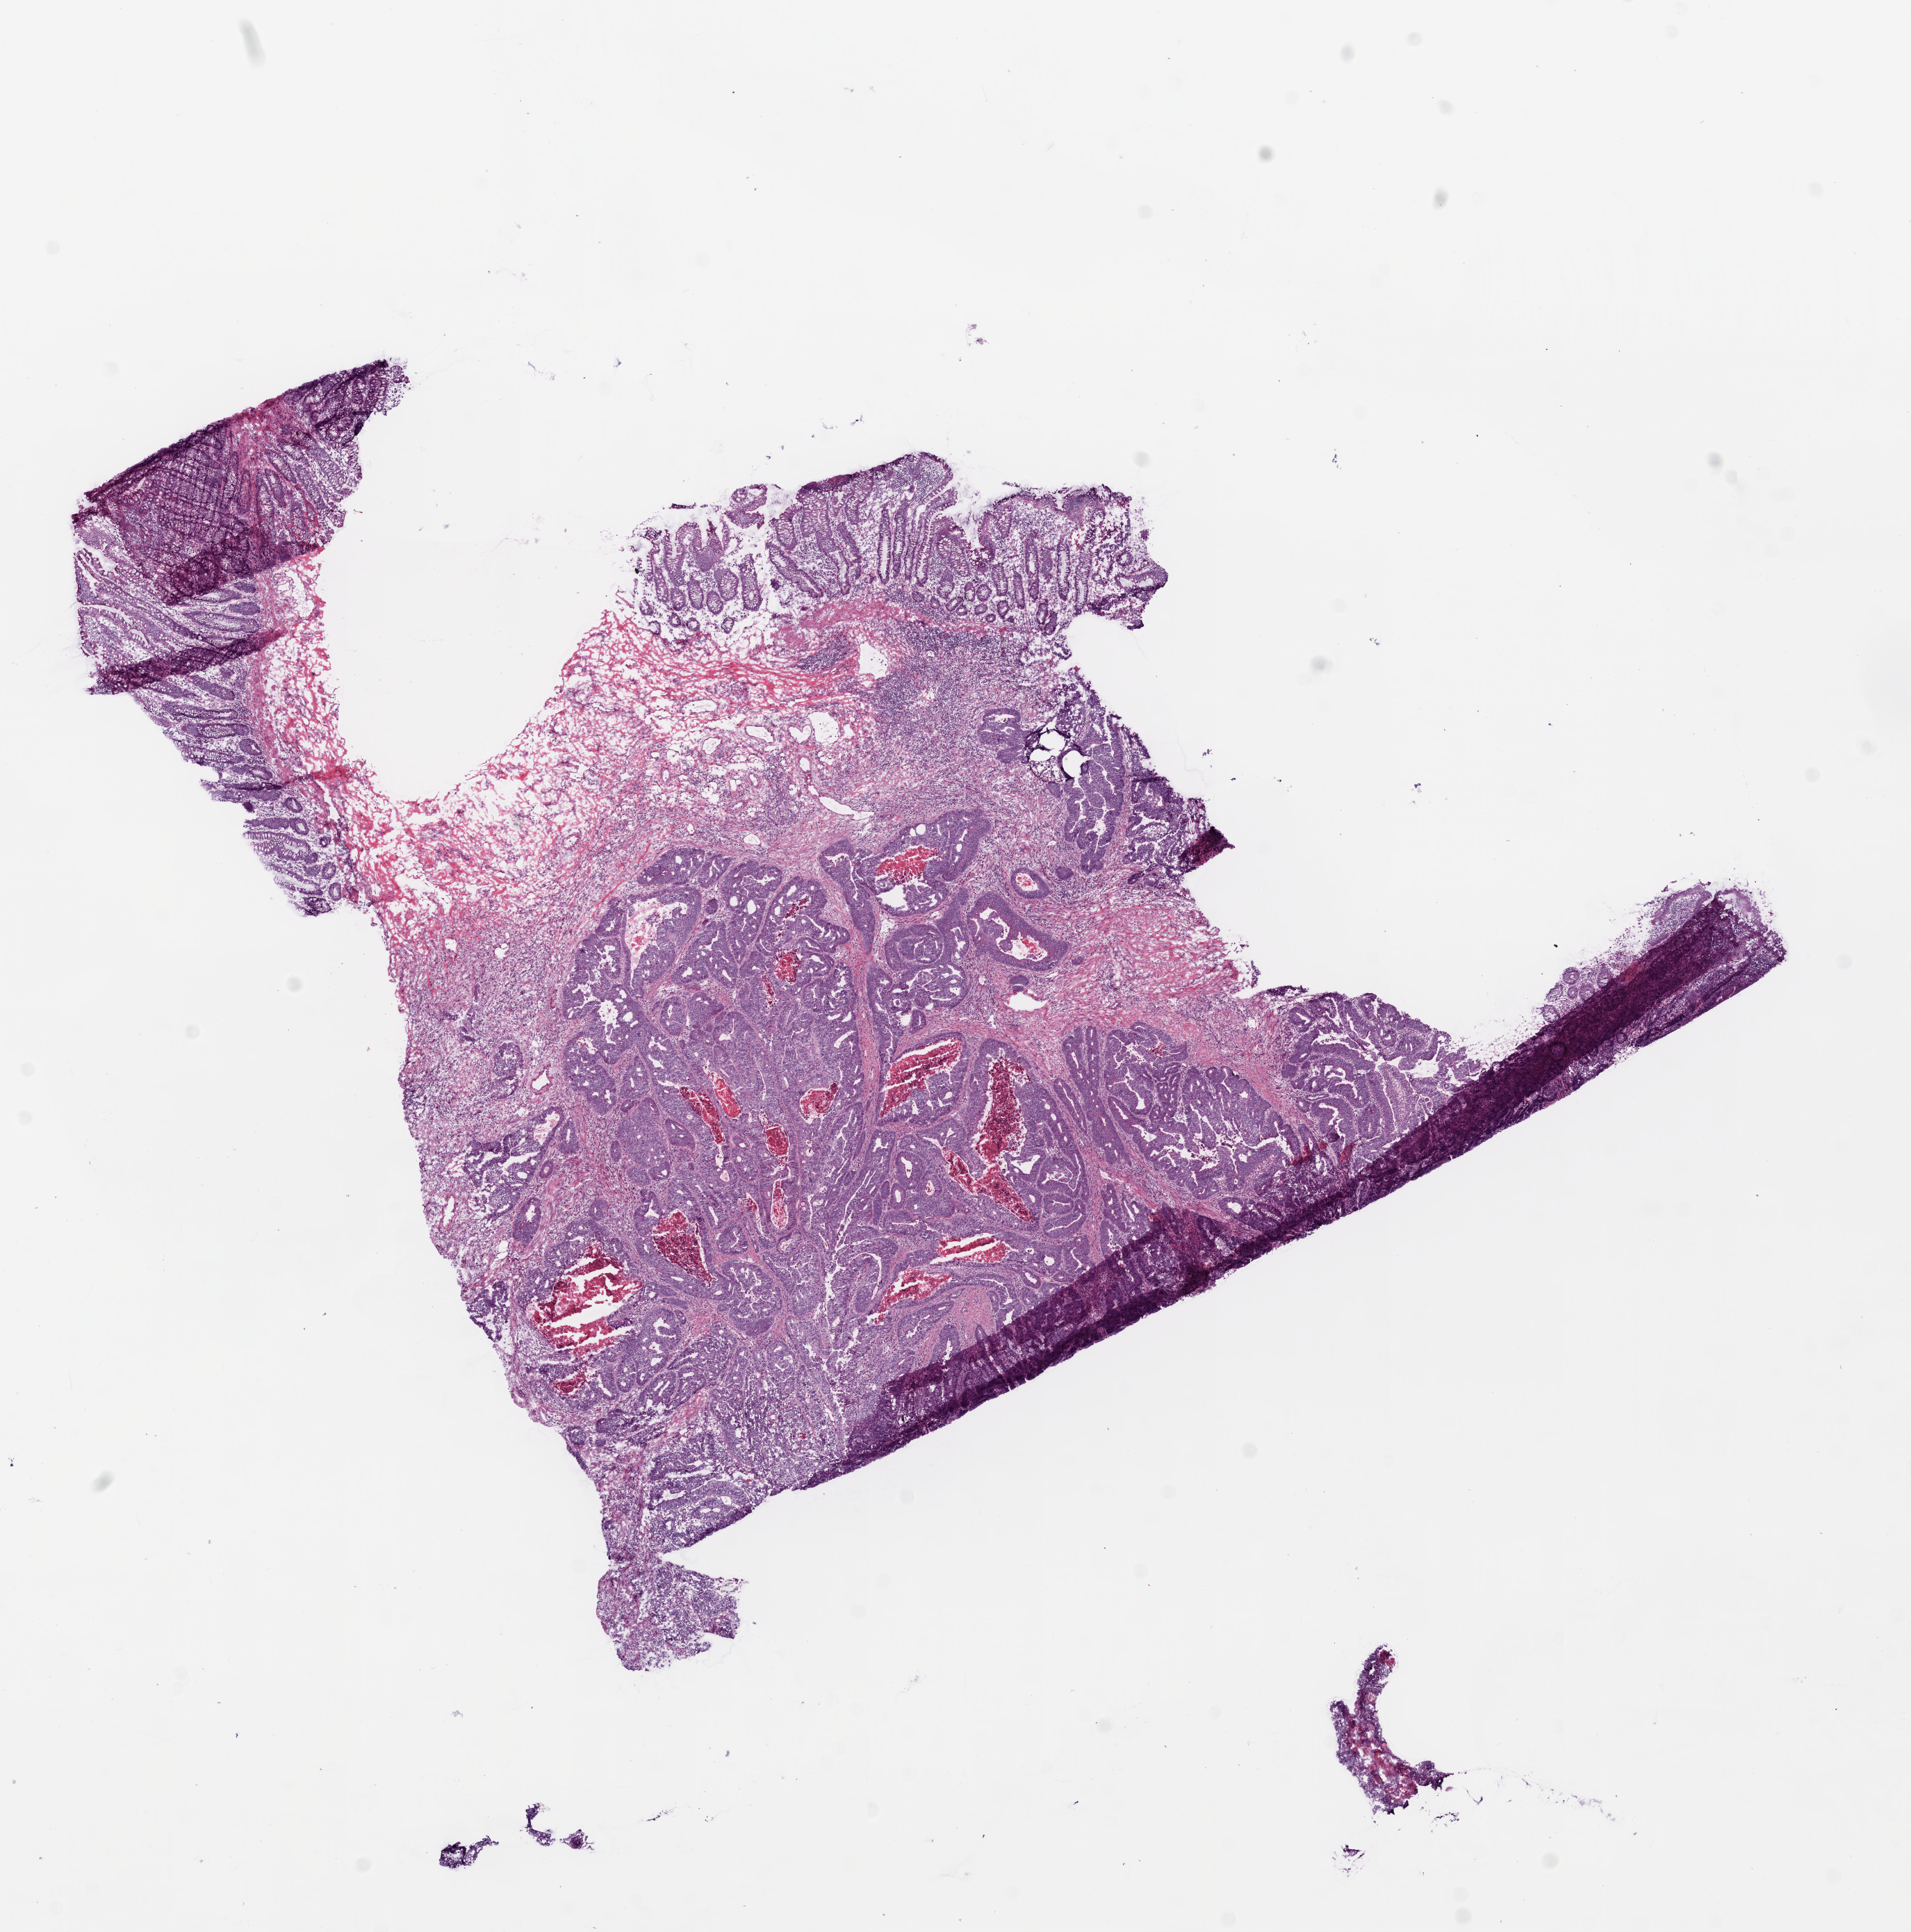
Whole-slide histology image, H&E — a low-resolution overview of the entire scanned area, about 11.0 x 11.2 mm (acquisition: 20x scan), frozen section, primary tumour sample from the colon. Patient: male, age at initial diagnosis 65 years. Pathologist review of this section (percent, as recorded): tumour cells 59%, tumour nuclei 60%, normal cells 25%, stromal cells 15%, necrosis 1%.
AJCC pathologic stage: IIA (6th edition). Pathologic diagnosis: Adenocarcinoma, NOS. Lymph nodes positive (case pathology): 0 of 36 examined.